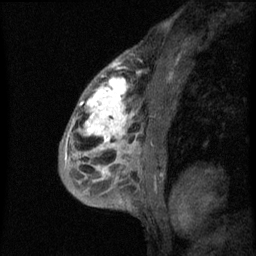
Breast MRI (dynamic contrast-enhanced), one sagittal slice. Position 37 of 60 along the scan axis. Dynamic contrast-enhanced series, image 2 of 3 at this slice position (ordered by acquisition). 1.5 T. TE 4.2 ms, TR 8 ms. 256 × 256 image matrix, field of view 180 × 180 mm. Patient: female, 50 years.
Outlined on this slice (semi-automatically segmented with operator editing):
- analysis volume of interest (the breast-tissue region the enhancement analysis was run in; not a lesion): bounding box (x1, y1, x2, y2) in pixels: (66, 64, 141, 187)
- tumour enhancement mask (voxels above the 70 % enhancement threshold inside the analysis volume of interest): (66, 64, 140, 177)